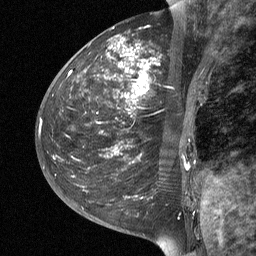
Breast MRI (dynamic contrast-enhanced), one sagittal slice. Slice 20 of 64 in the series (ordered by position). Dynamic contrast-enhanced study with each time point stored as its own series, time point 2 of 3 at this slice position (early post-contrast, ordered by acquisition time). 1.5 T. TE 4.8 ms, TR 27 ms. 2 mm slice thickness. 256 × 256 image matrix. Patient: female, 42 years. From the clinical record (not read from this slice): setting: breast cancer imaged before/during neoadjuvant chemotherapy; receptor status: triple-negative.
Annotated regions visible in this slice (semi-automatically segmented with operator editing):
- analysis volume of interest (the breast-tissue region the enhancement analysis was run in; not a lesion): bounding box <43,29,203,190> (left, top, right, bottom; pixels)
- tumour enhancement mask (voxels above the 90 % enhancement threshold inside the analysis volume of interest): <70,46,156,99>